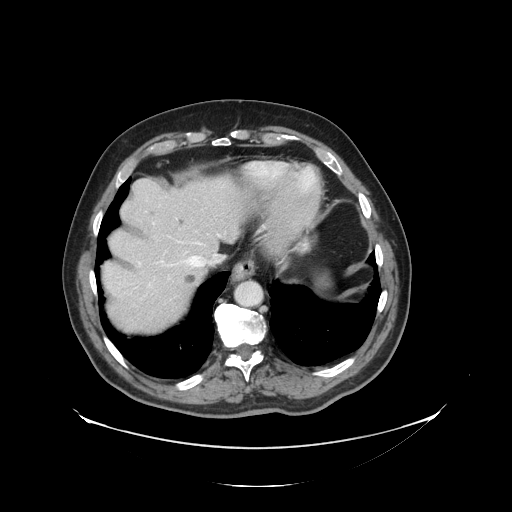
Contrast-enhanced abdominal CT, one axial slice; slice 114 of 138 in the series (ordered by position); intravenous contrast given; soft-tissue window (W 400 / L 40 HU); 512 × 512 image matrix. Male patient, age 77 years. Case-level facts recorded for this patient, not image findings: diagnosis: colorectal cancer liver metastases, imaged before liver resection; multiple liver metastases: no; largest metastasis: 1.5 cm; disease in both lobes: no.
Annotated regions visible in this slice (outlined manually by an expert reader):
- hepatic veins: box from (x=137, y=233) to (x=221, y=287) px
- liver: (x=103, y=176)–(x=248, y=332)
- planned liver remnant (the part of the liver to remain after resection): (x=104, y=176)–(x=243, y=290)
- liver metastasis: (x=185, y=275)–(x=196, y=284)